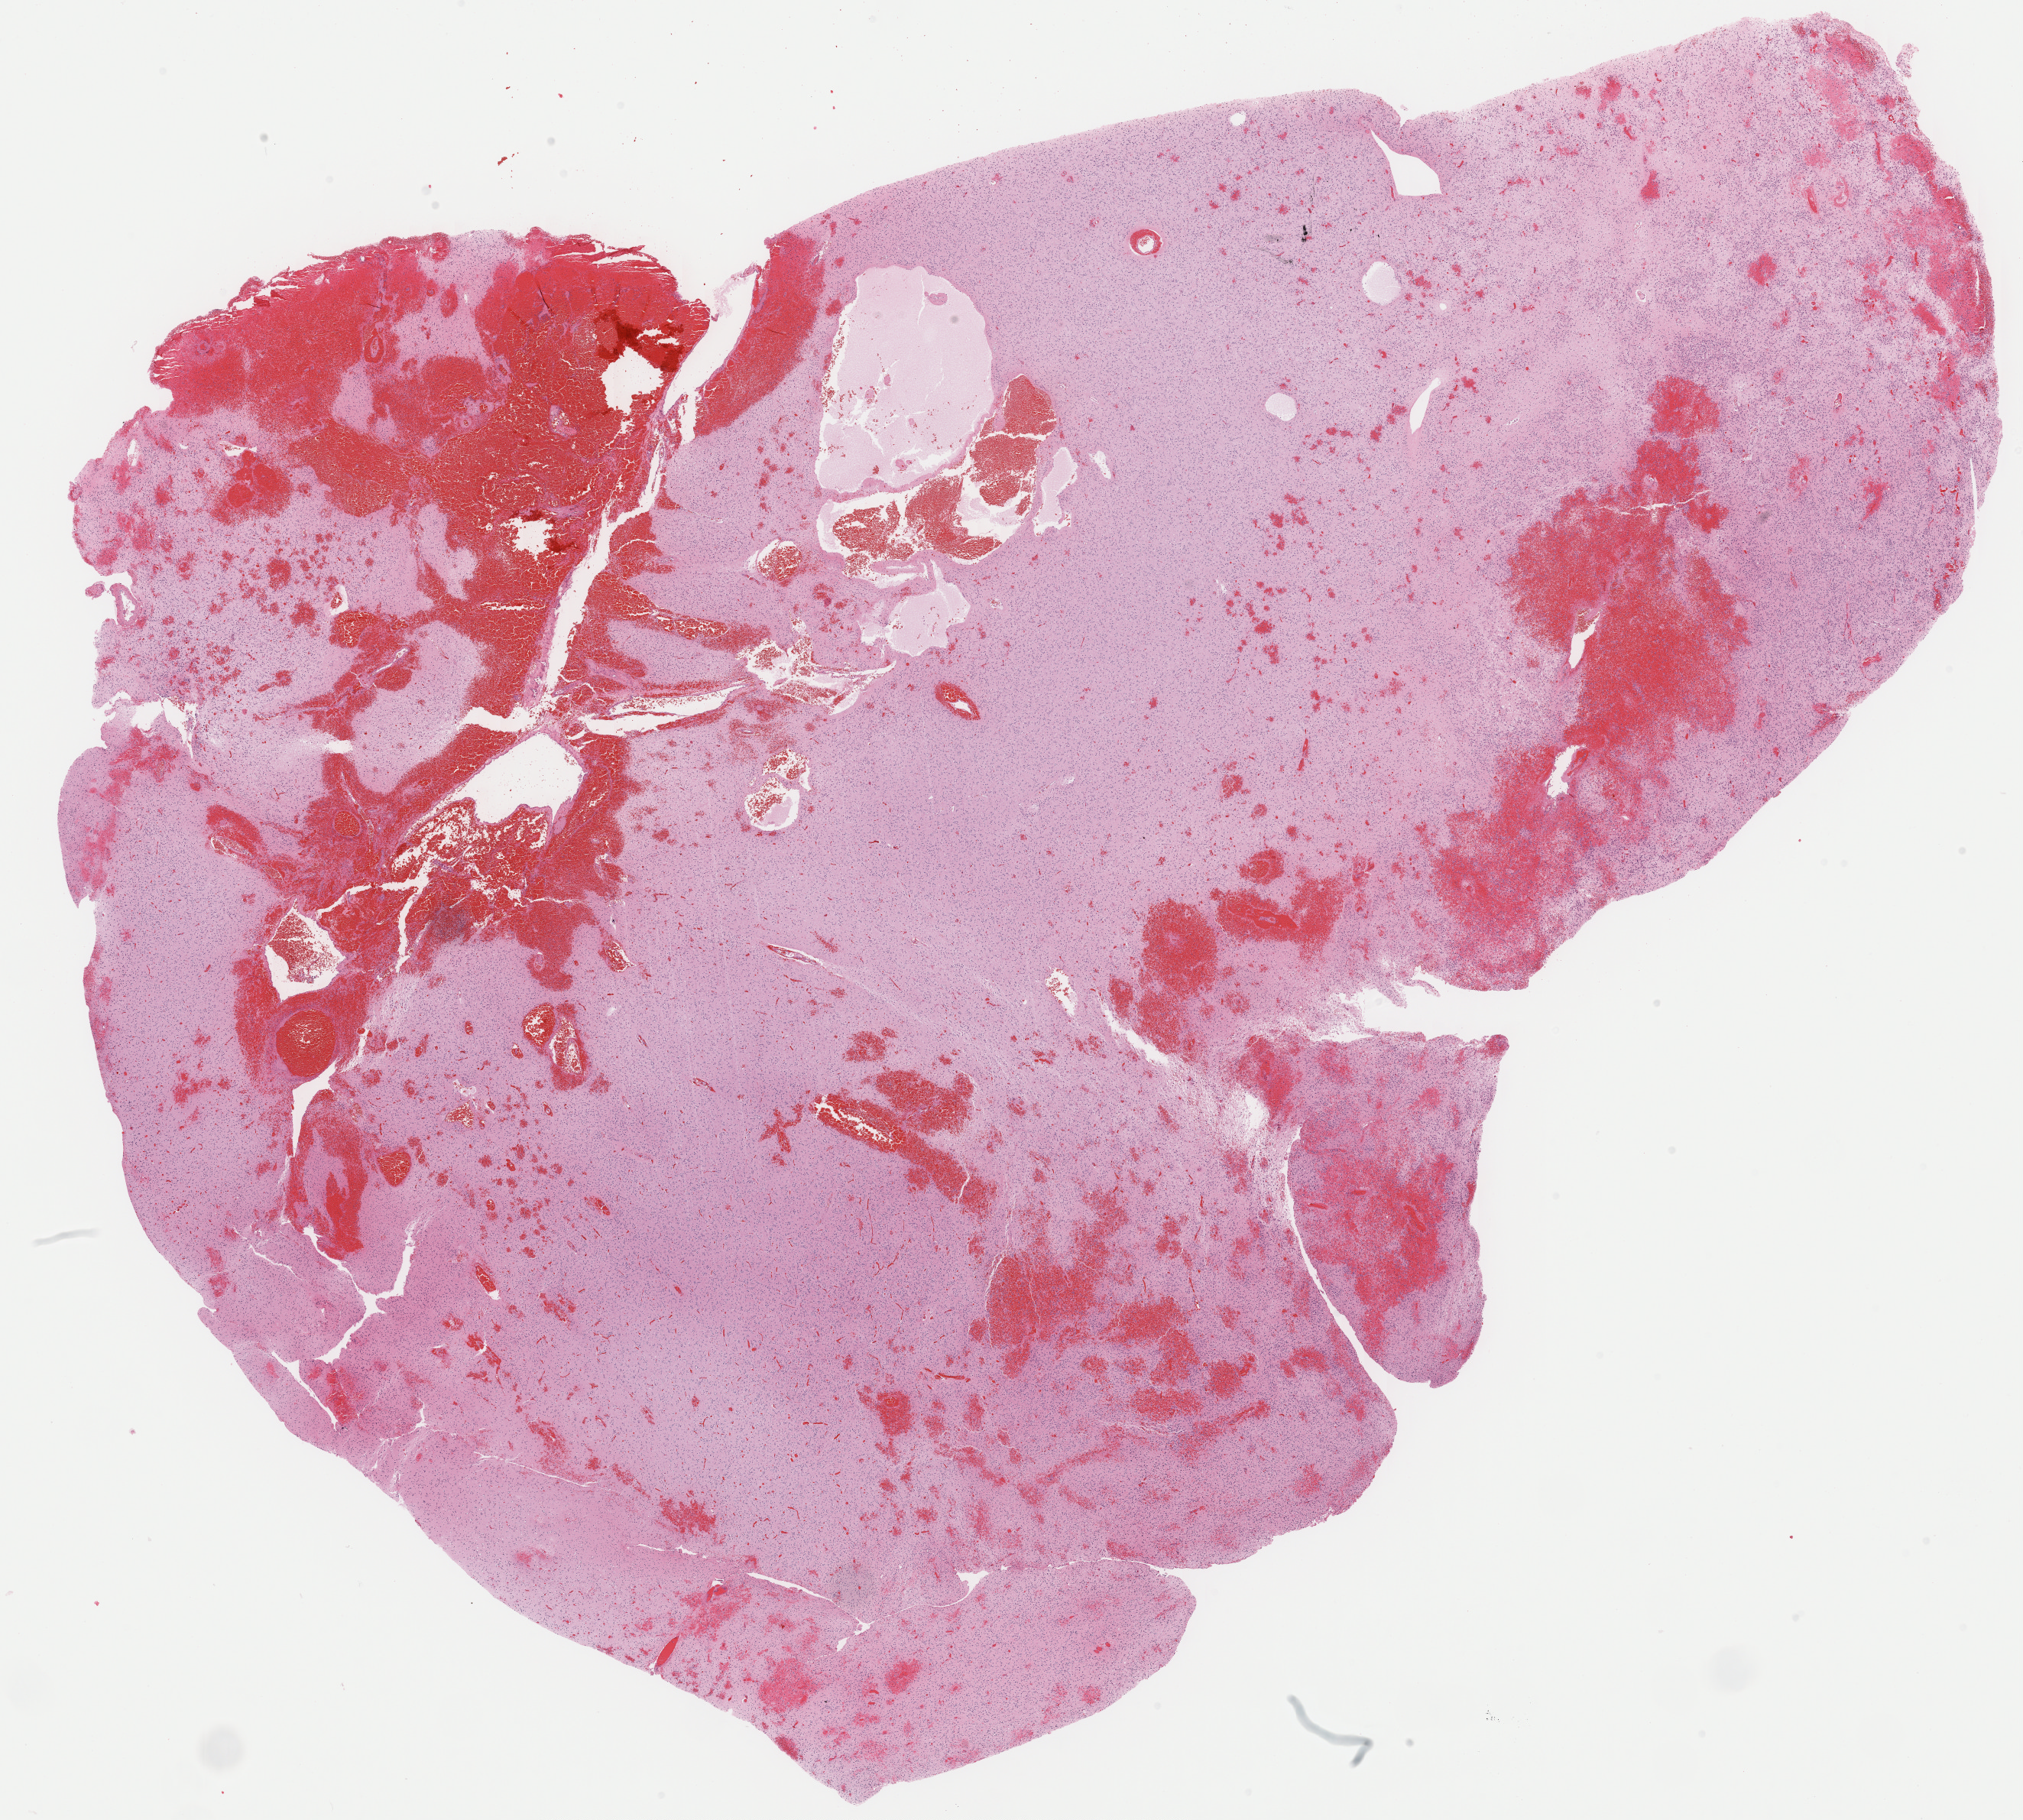
Digitized H&E tissue section (whole slide) — whole scanned area (about 20.9 x 18.8 mm, acquisition: 40x scan) shown as a low-resolution overview, formalin-fixed paraffin-embedded (FFPE) diagnostic section, primary tumour sample from the brain. Male, age 59 years at initial diagnosis. Histologic grade: G2 (moderately differentiated).
* diagnosis: Oligodendroglioma, NOS (cerebrum)